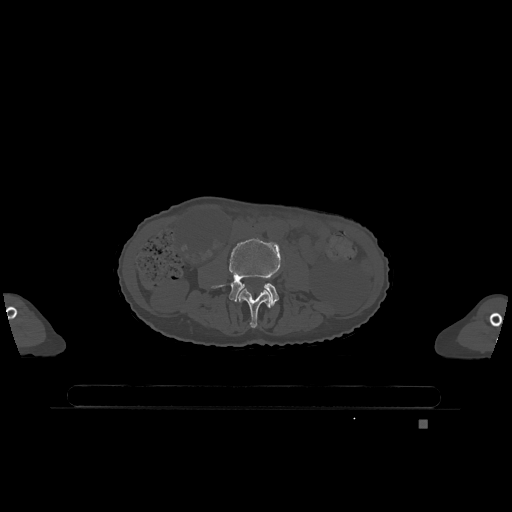
CT including the spine, one axial slice. Position 325 of 1317 along the scan axis. Bone window (W 1800 / L 400 HU). 512 × 512 image matrix. Patient: female, 74 years. Case-level facts recorded for this patient, not image findings: primary cancer: lung; vertebrae with lytic lesions (as recorded): T1, T4, T5, T6, L4, L5.
Structures marked on this image (semi-automatic segmentation, software-assisted and operator-edited):
- L3 vertebra: bounding box (x1, y1, x2, y2) in pixels: (238, 288, 271, 328)
- L4 vertebra: (212, 238, 281, 306)